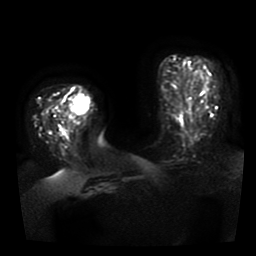
Breast MRI, one axial slice; position 15 of 41 along the scan axis; diffusion-weighted series; image 2 of 4 stored at this slice position (different b-values; order by instance number); 1.5 T; 256 × 256 image matrix, field of view 330 × 330 mm. Female patient.
Annotated regions visible in this slice (outlined manually by an expert reader):
- tumour on diffusion-weighted imaging: bounding box [x1, y1, x2, y2] px = [65, 94, 89, 119]